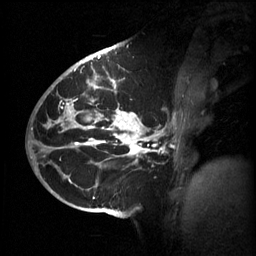
Breast MRI (dynamic contrast-enhanced), one sagittal slice. Position 32 of 60 along the scan axis. 3 images stored at this slice position (order not interpretable as contrast timing). 1.5 T. TE 4.2 ms, TR 11 ms. 256 × 256 image matrix, field of view 220 × 220 mm. Patient: female, 51 years.
Annotated regions visible in this slice (semi-automatically segmented with operator editing):
- analysis volume of interest (the breast-tissue region the enhancement analysis was run in; not a lesion): bounding box [x1, y1, x2, y2] px = [63, 80, 183, 201]
- tumour enhancement mask (voxels above the 70 % enhancement threshold inside the analysis volume of interest): [63, 80, 165, 199]